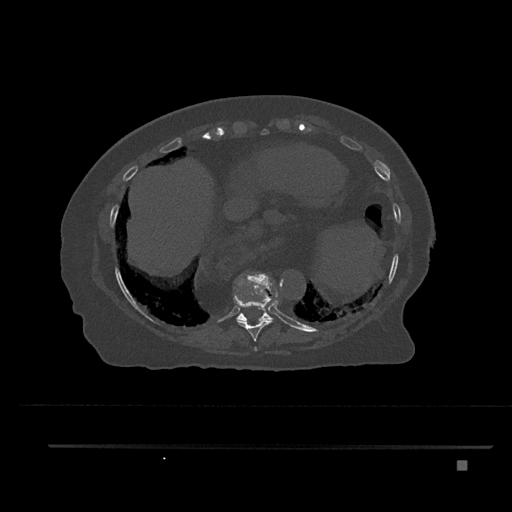
CT including the spine, one axial slice. Slice 382 of 797 in the series (ordered by position). 120 kVp. Bone window (W 1800 / L 400 HU). 0.5 mm slice thickness. 512 × 512 image matrix, field of view 437 × 437 mm. Female patient, age 76 years. From the clinical record (not read from this slice): primary cancer: lung; vertebrae with lytic lesions (as recorded): T11, L3.
Annotated regions visible in this slice (semi-automatically segmented with operator editing):
- T10 vertebra: bounding box <236,275,274,322> (left, top, right, bottom; pixels)
- T8 vertebra: <254,347,258,351>
- T9 vertebra: <233,272,278,341>